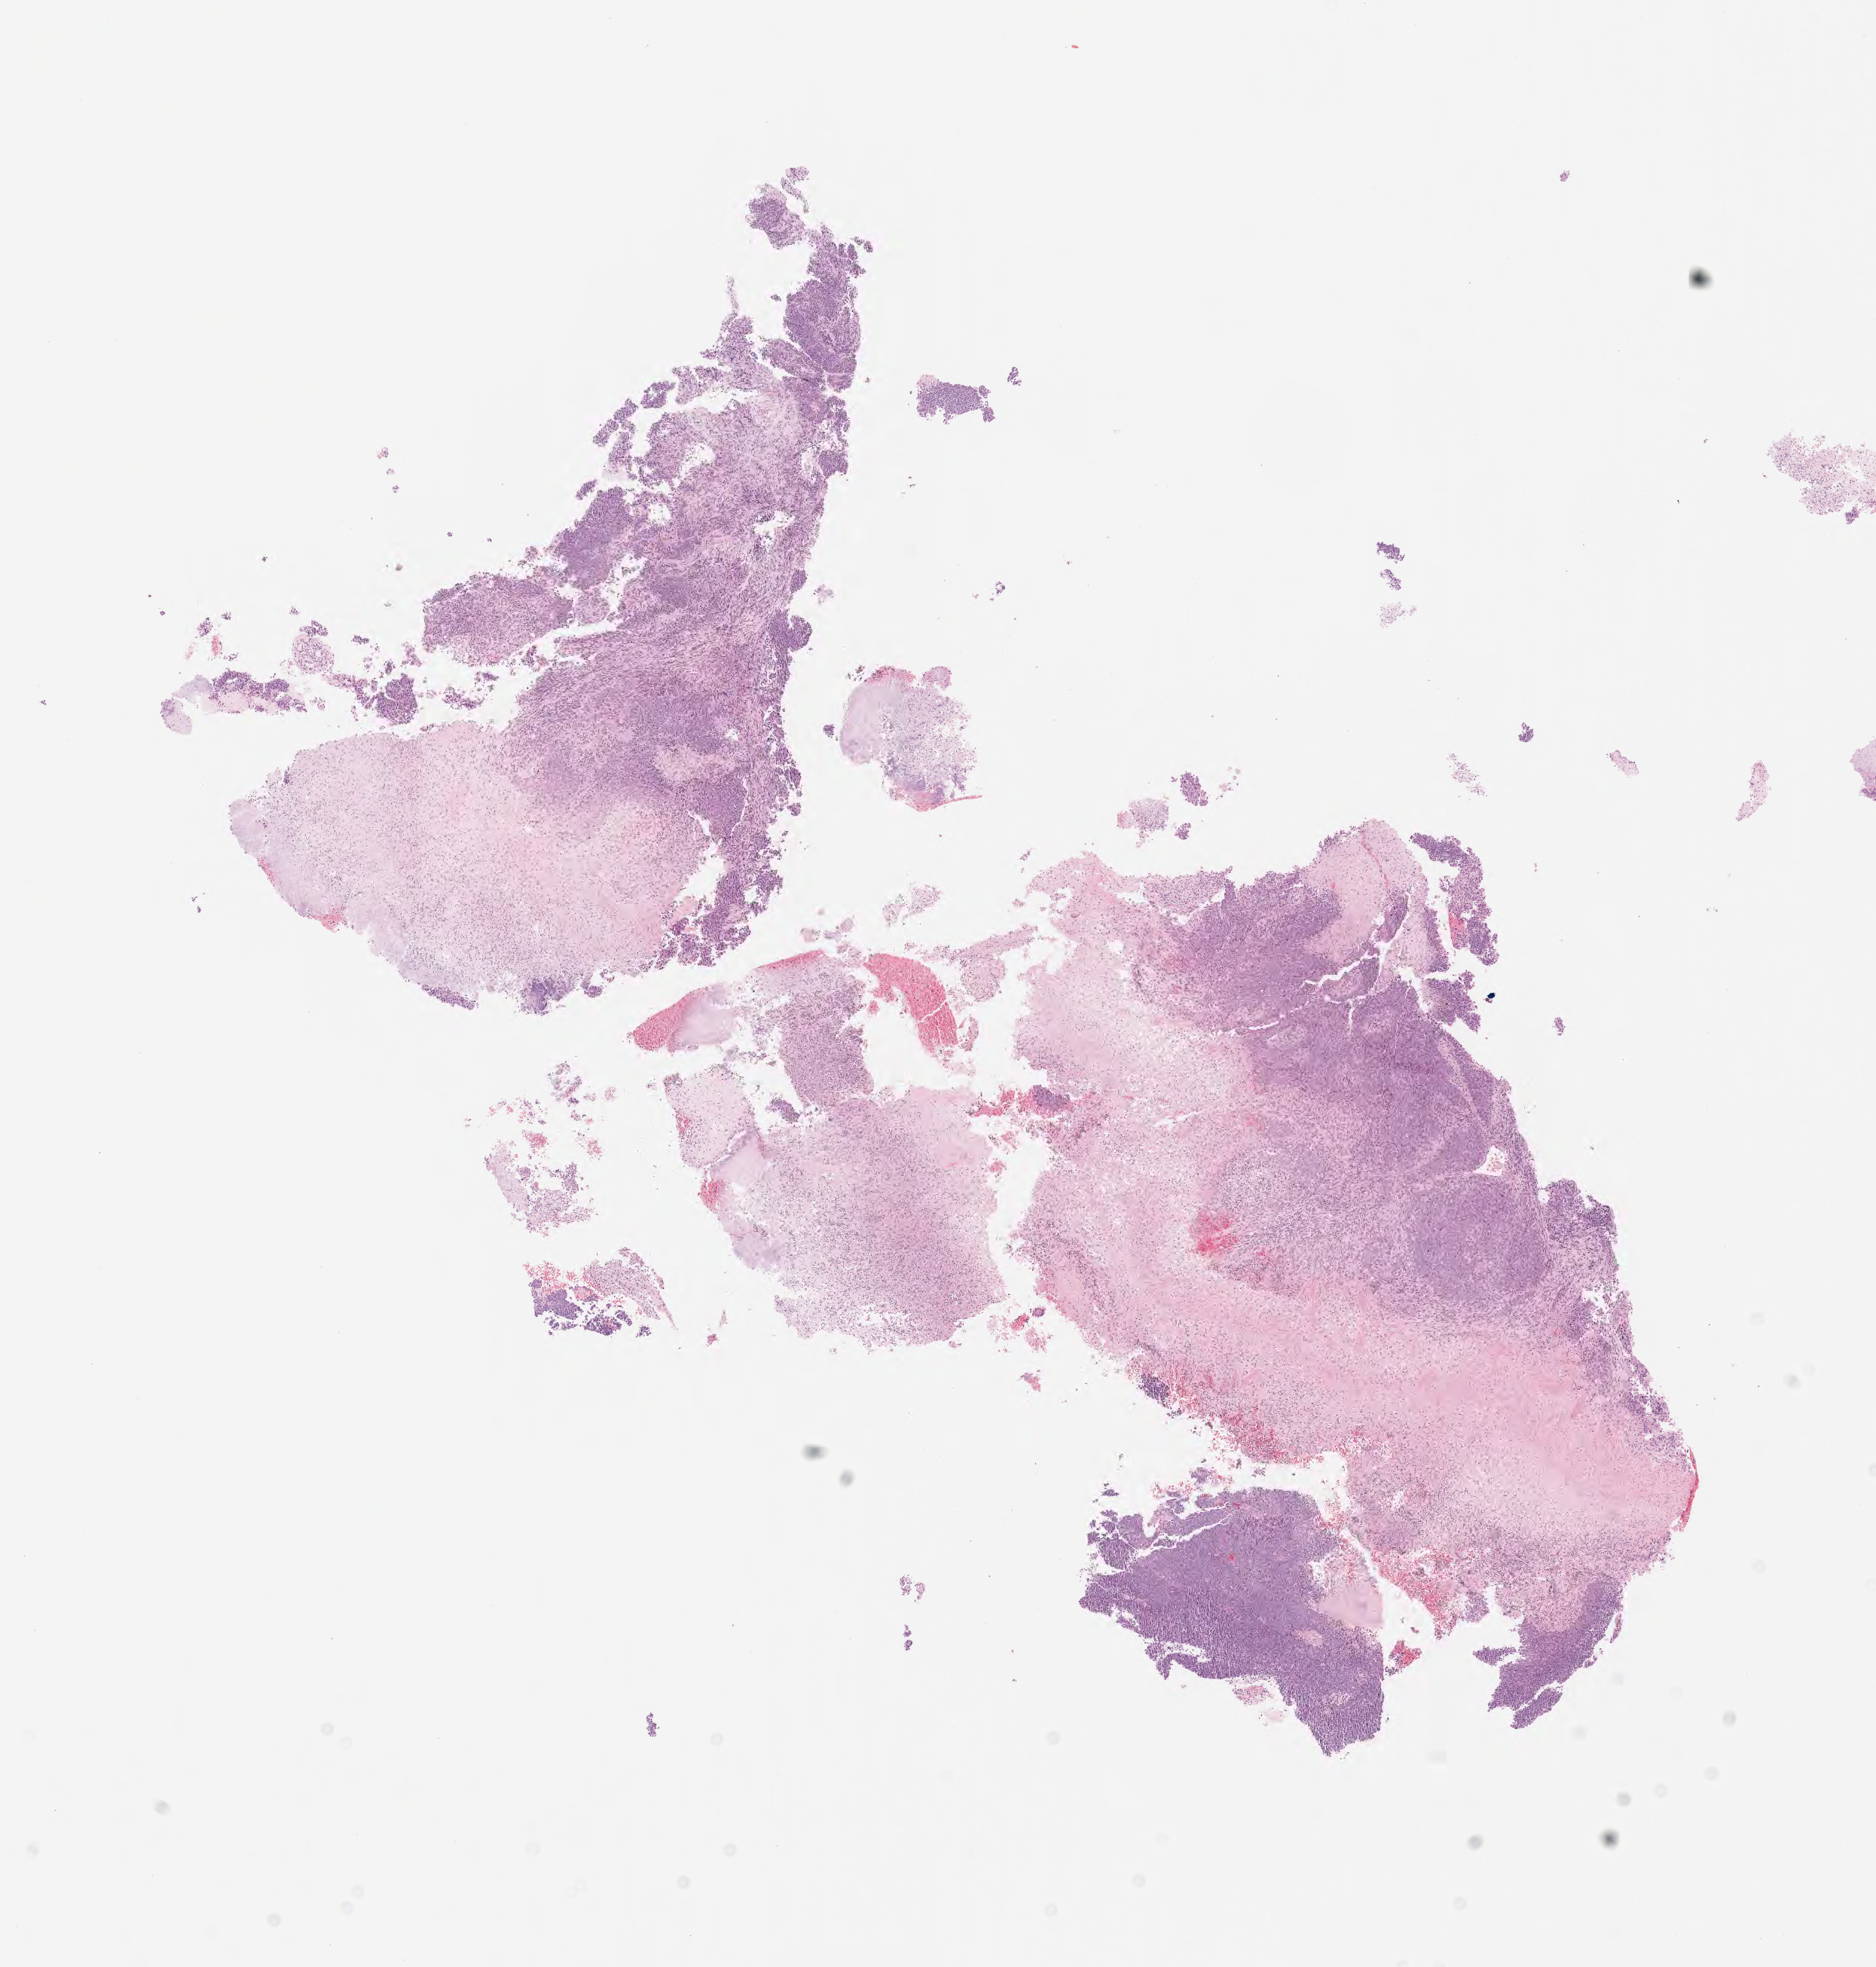
Whole-slide image, haematoxylin and eosin stain — a low-resolution overview of the entire scanned area, about 10.1 x 10.5 mm, tumor tissue, anatomic site: cervix. Female patient, 65 years old.
Histologic diagnosis: Squamous cell carcinoma, large cell, nonkeratinizing, NOS.